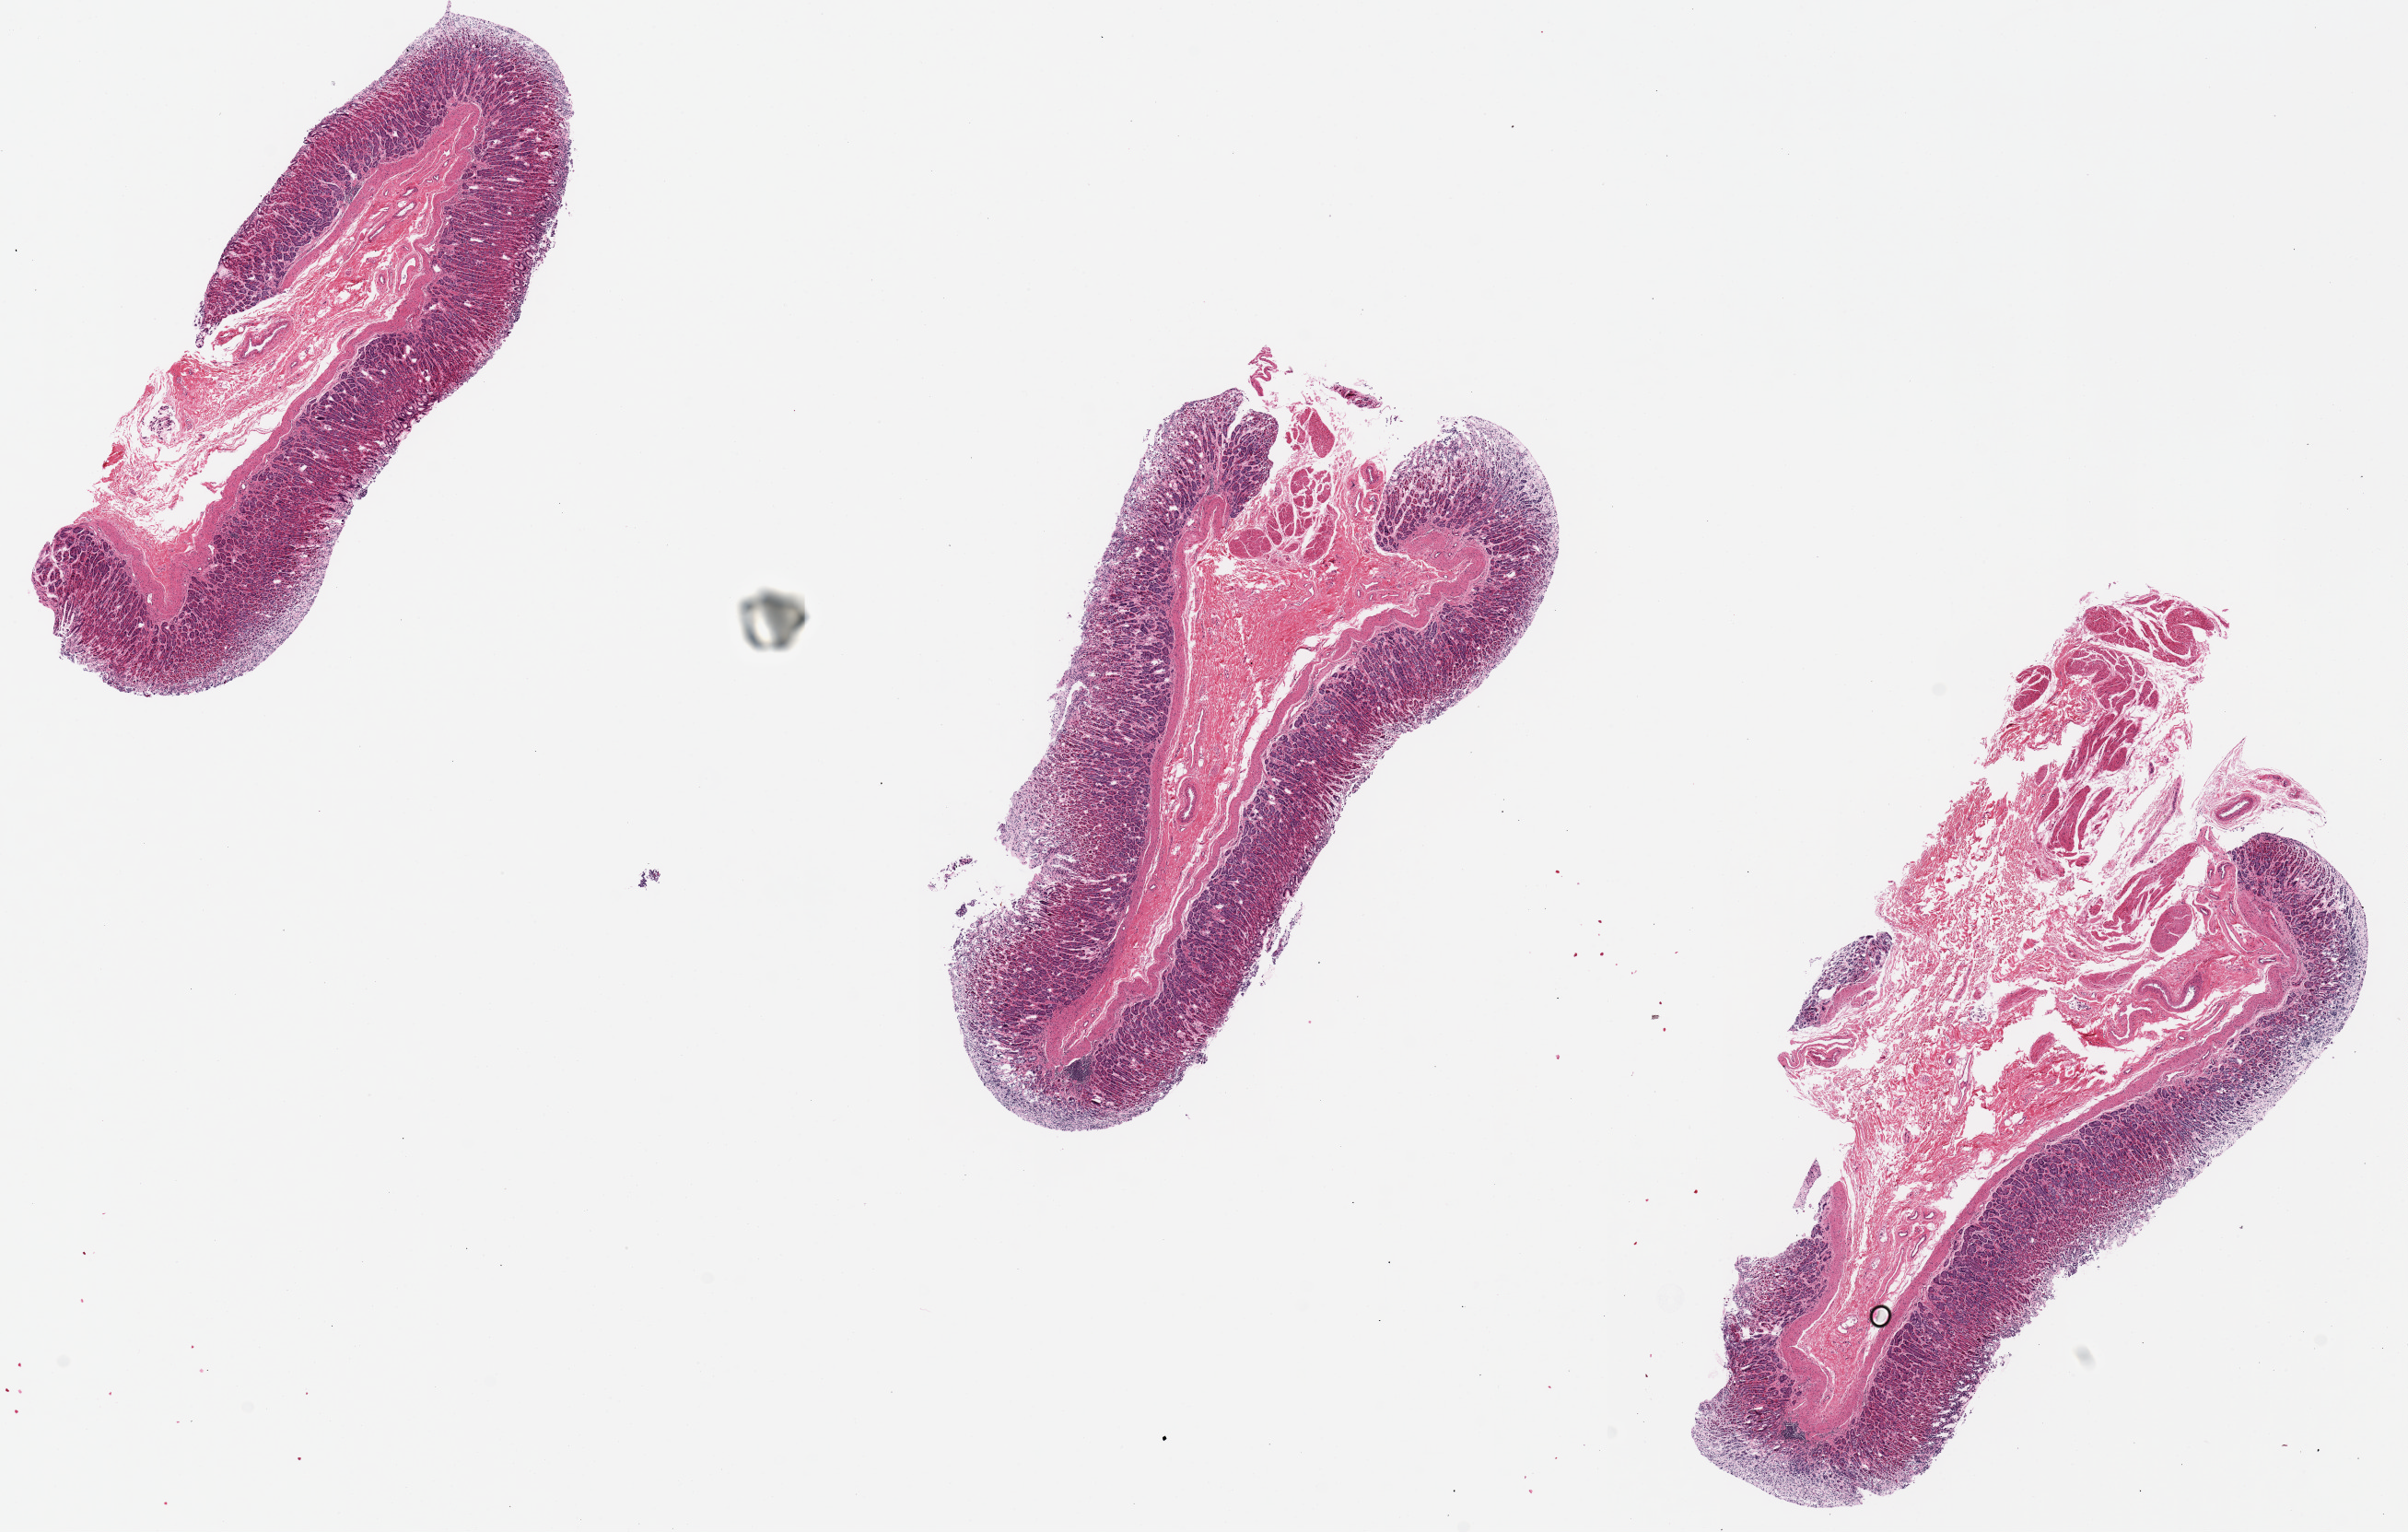
Whole-slide image, haematoxylin and eosin stain — low-resolution overview of the scanned area, about 20.7 x 13.2 mm (slide scanned at 20x). PAXgene-fixed, paraffin-embedded tissue. Section of stomach (target tissue). Tissue donor sample. Donor sex: male.
Review note (as recorded): Mucosa is ~25% of specimen thickness.